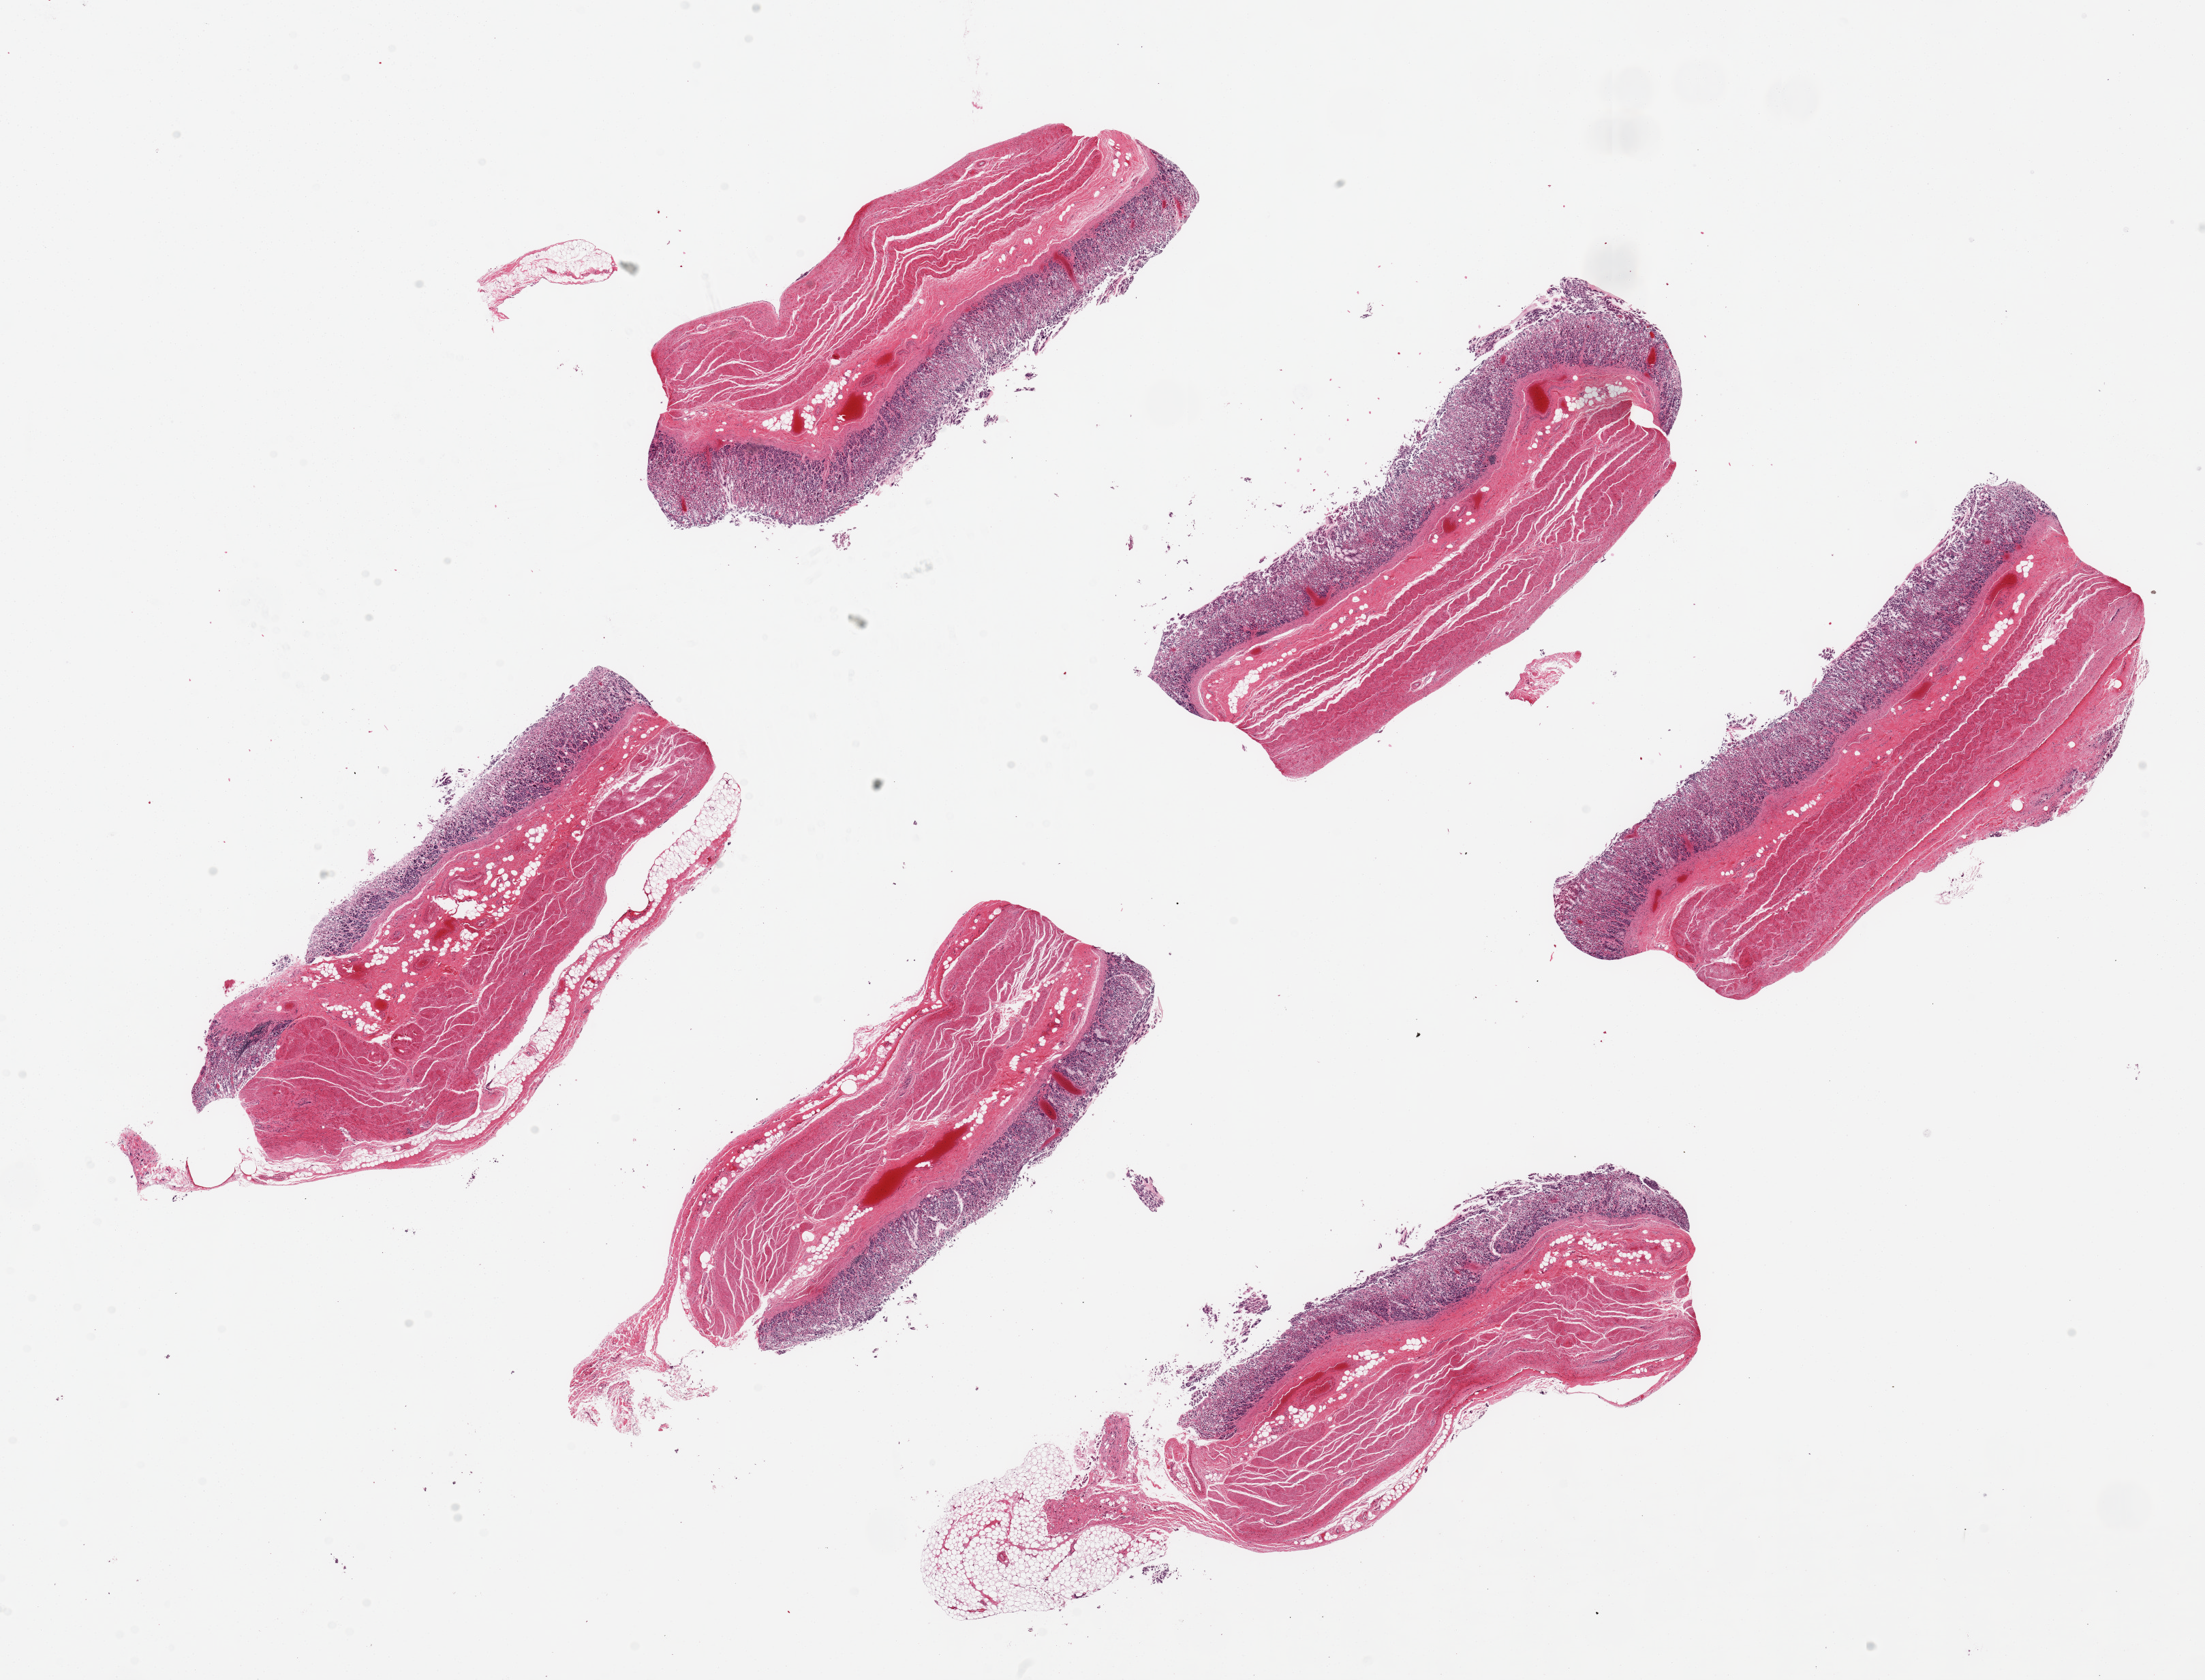
Whole-slide image, H&E stain, a low-resolution overview of the entire scanned area, about 25.6 x 19.5 mm. PAXgene-fixed paraffin-embedded (PFPE) section. Sampled site (target tissue): stomach. Tissue donor sample. Donor sex: male.
Review note (as recorded): 6 ~6.5x2.5mm pieces. Mucosa is 20-25% of thickness, but epithelial component badly autolyzed.